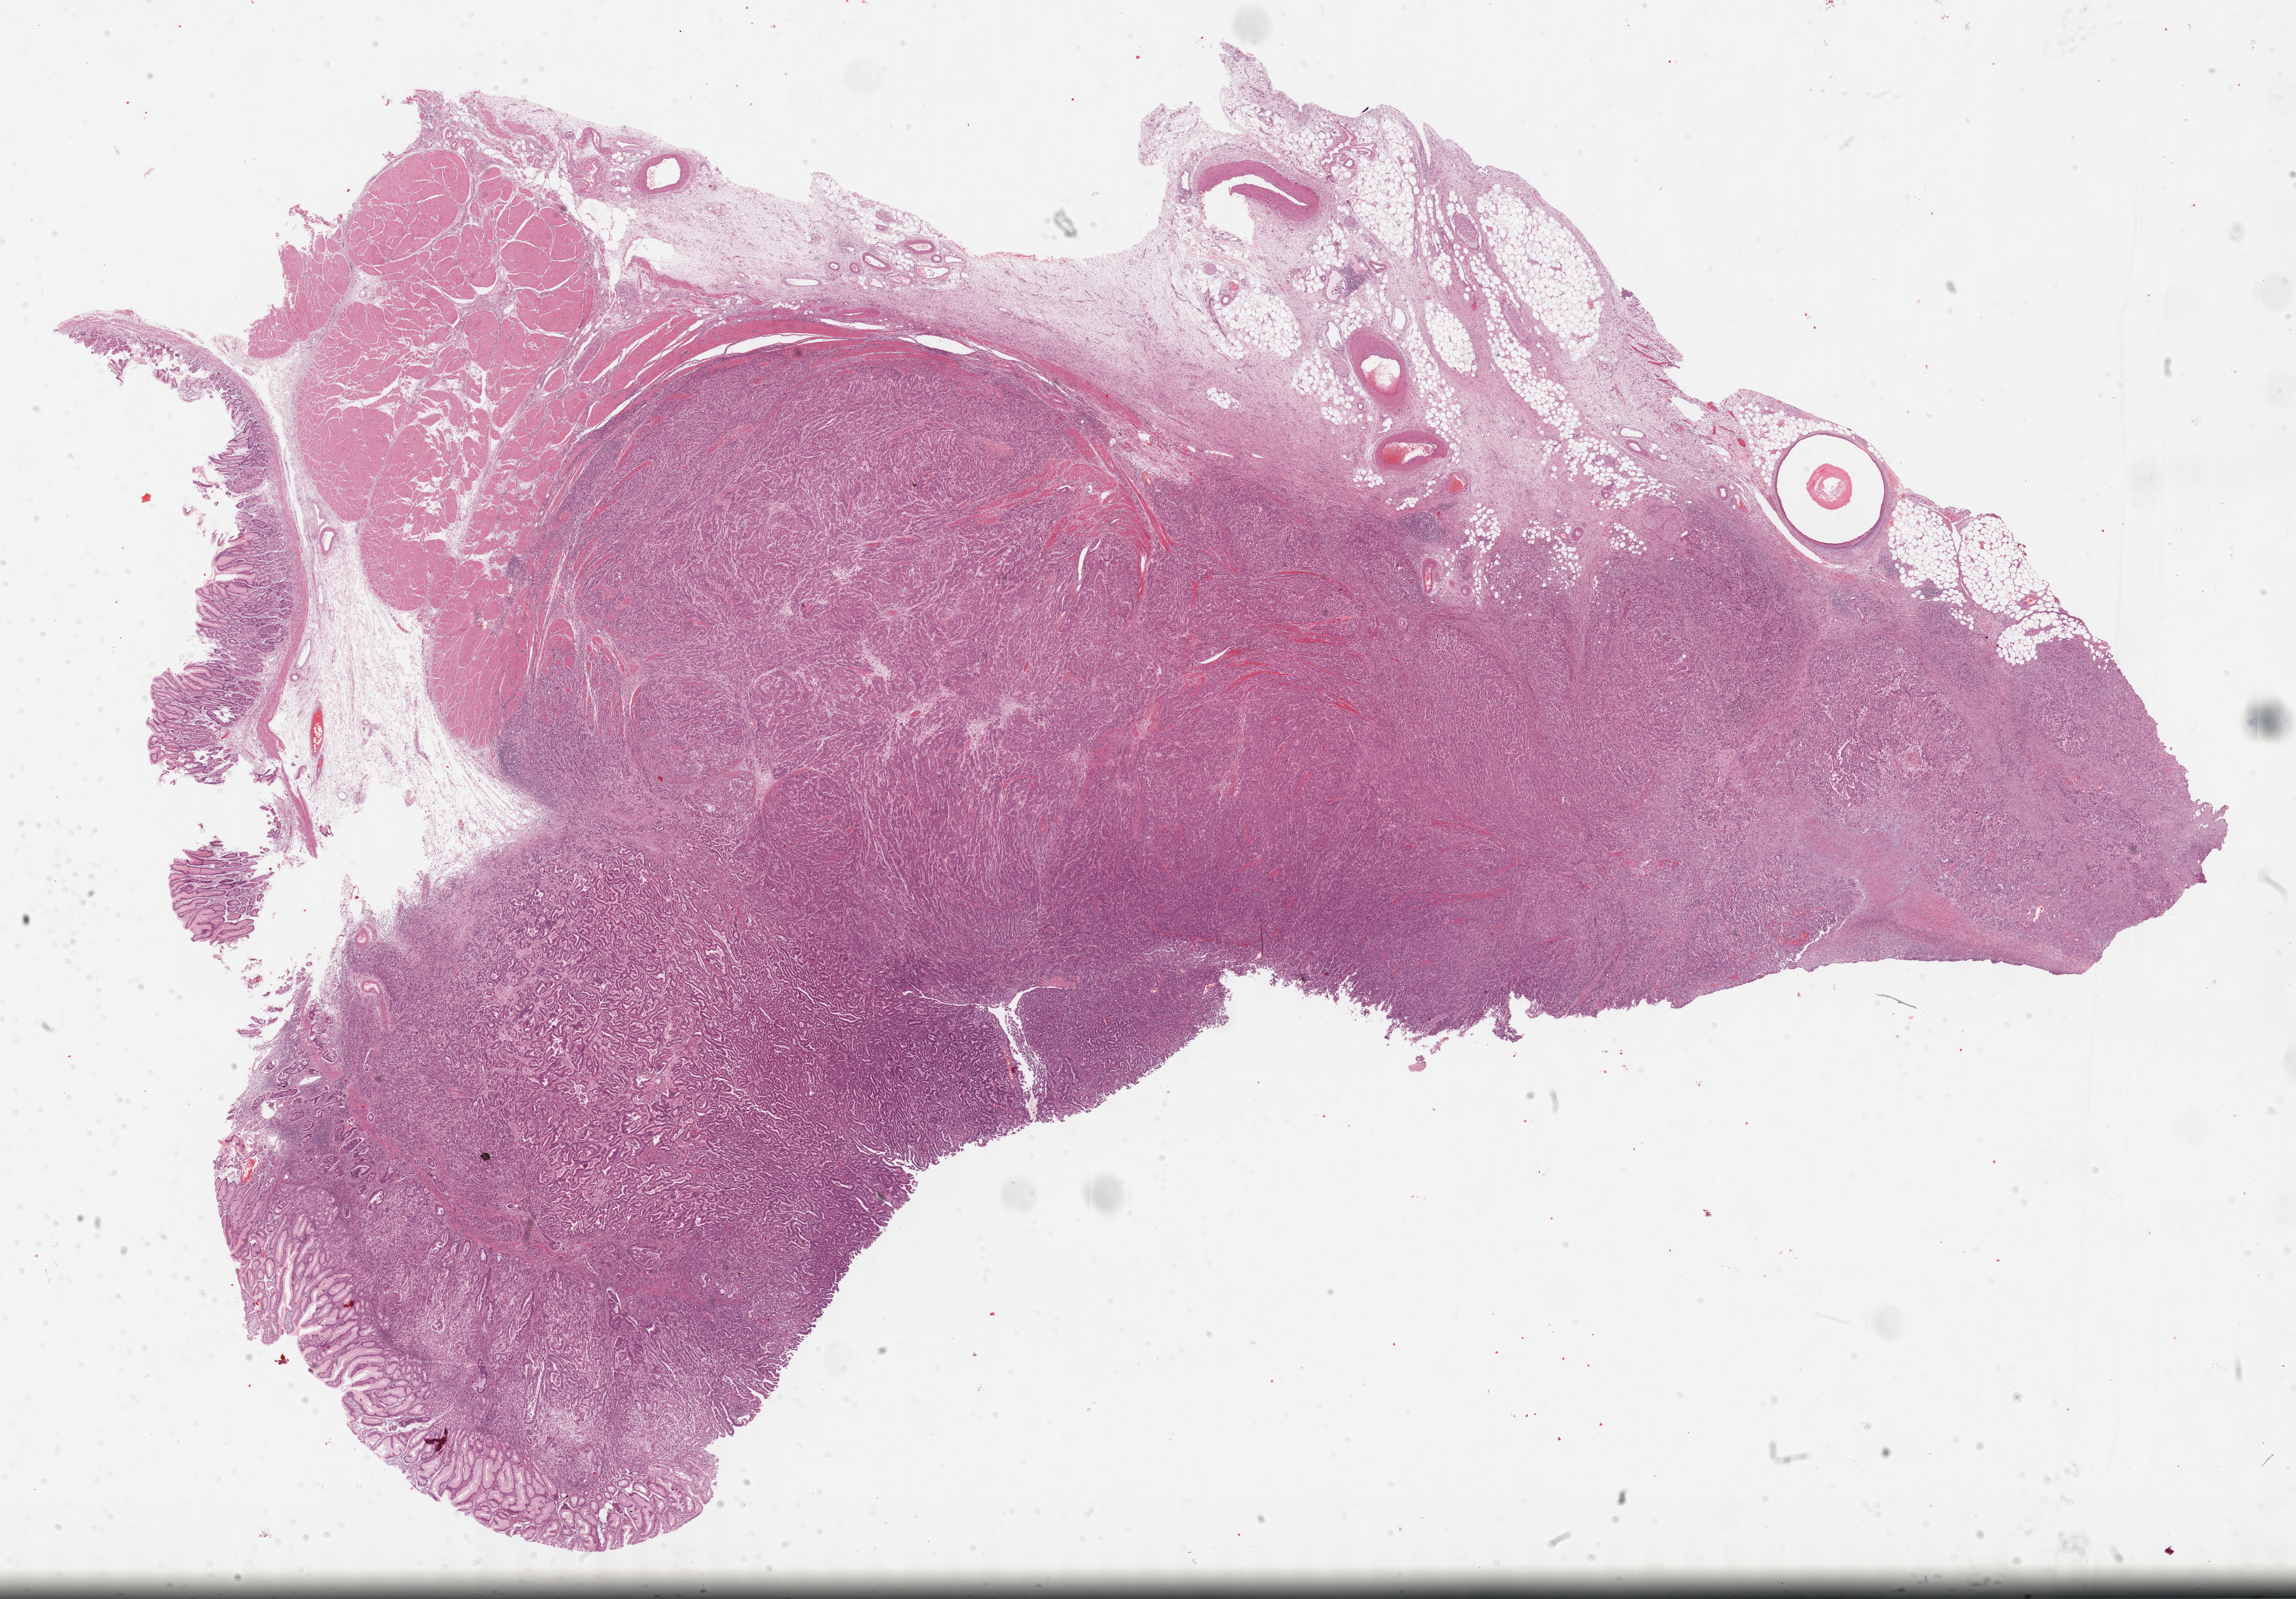
Hematoxylin and eosin (H&E) stained whole-slide image, low-resolution overview of the scanned area, about 29.7 x 20.7 mm (from a 40x scan); formalin-fixed paraffin-embedded (FFPE) diagnostic section; primary tumour sample from the stomach. Patient: female, age at initial diagnosis 72 years. Histologic grade: G3 (poorly differentiated).
* diagnosis: Tubular adenocarcinoma
* lymph nodes positive (case pathology): 13 of 18 examined
* AJCC pathologic stage: IIIB (7th edition)